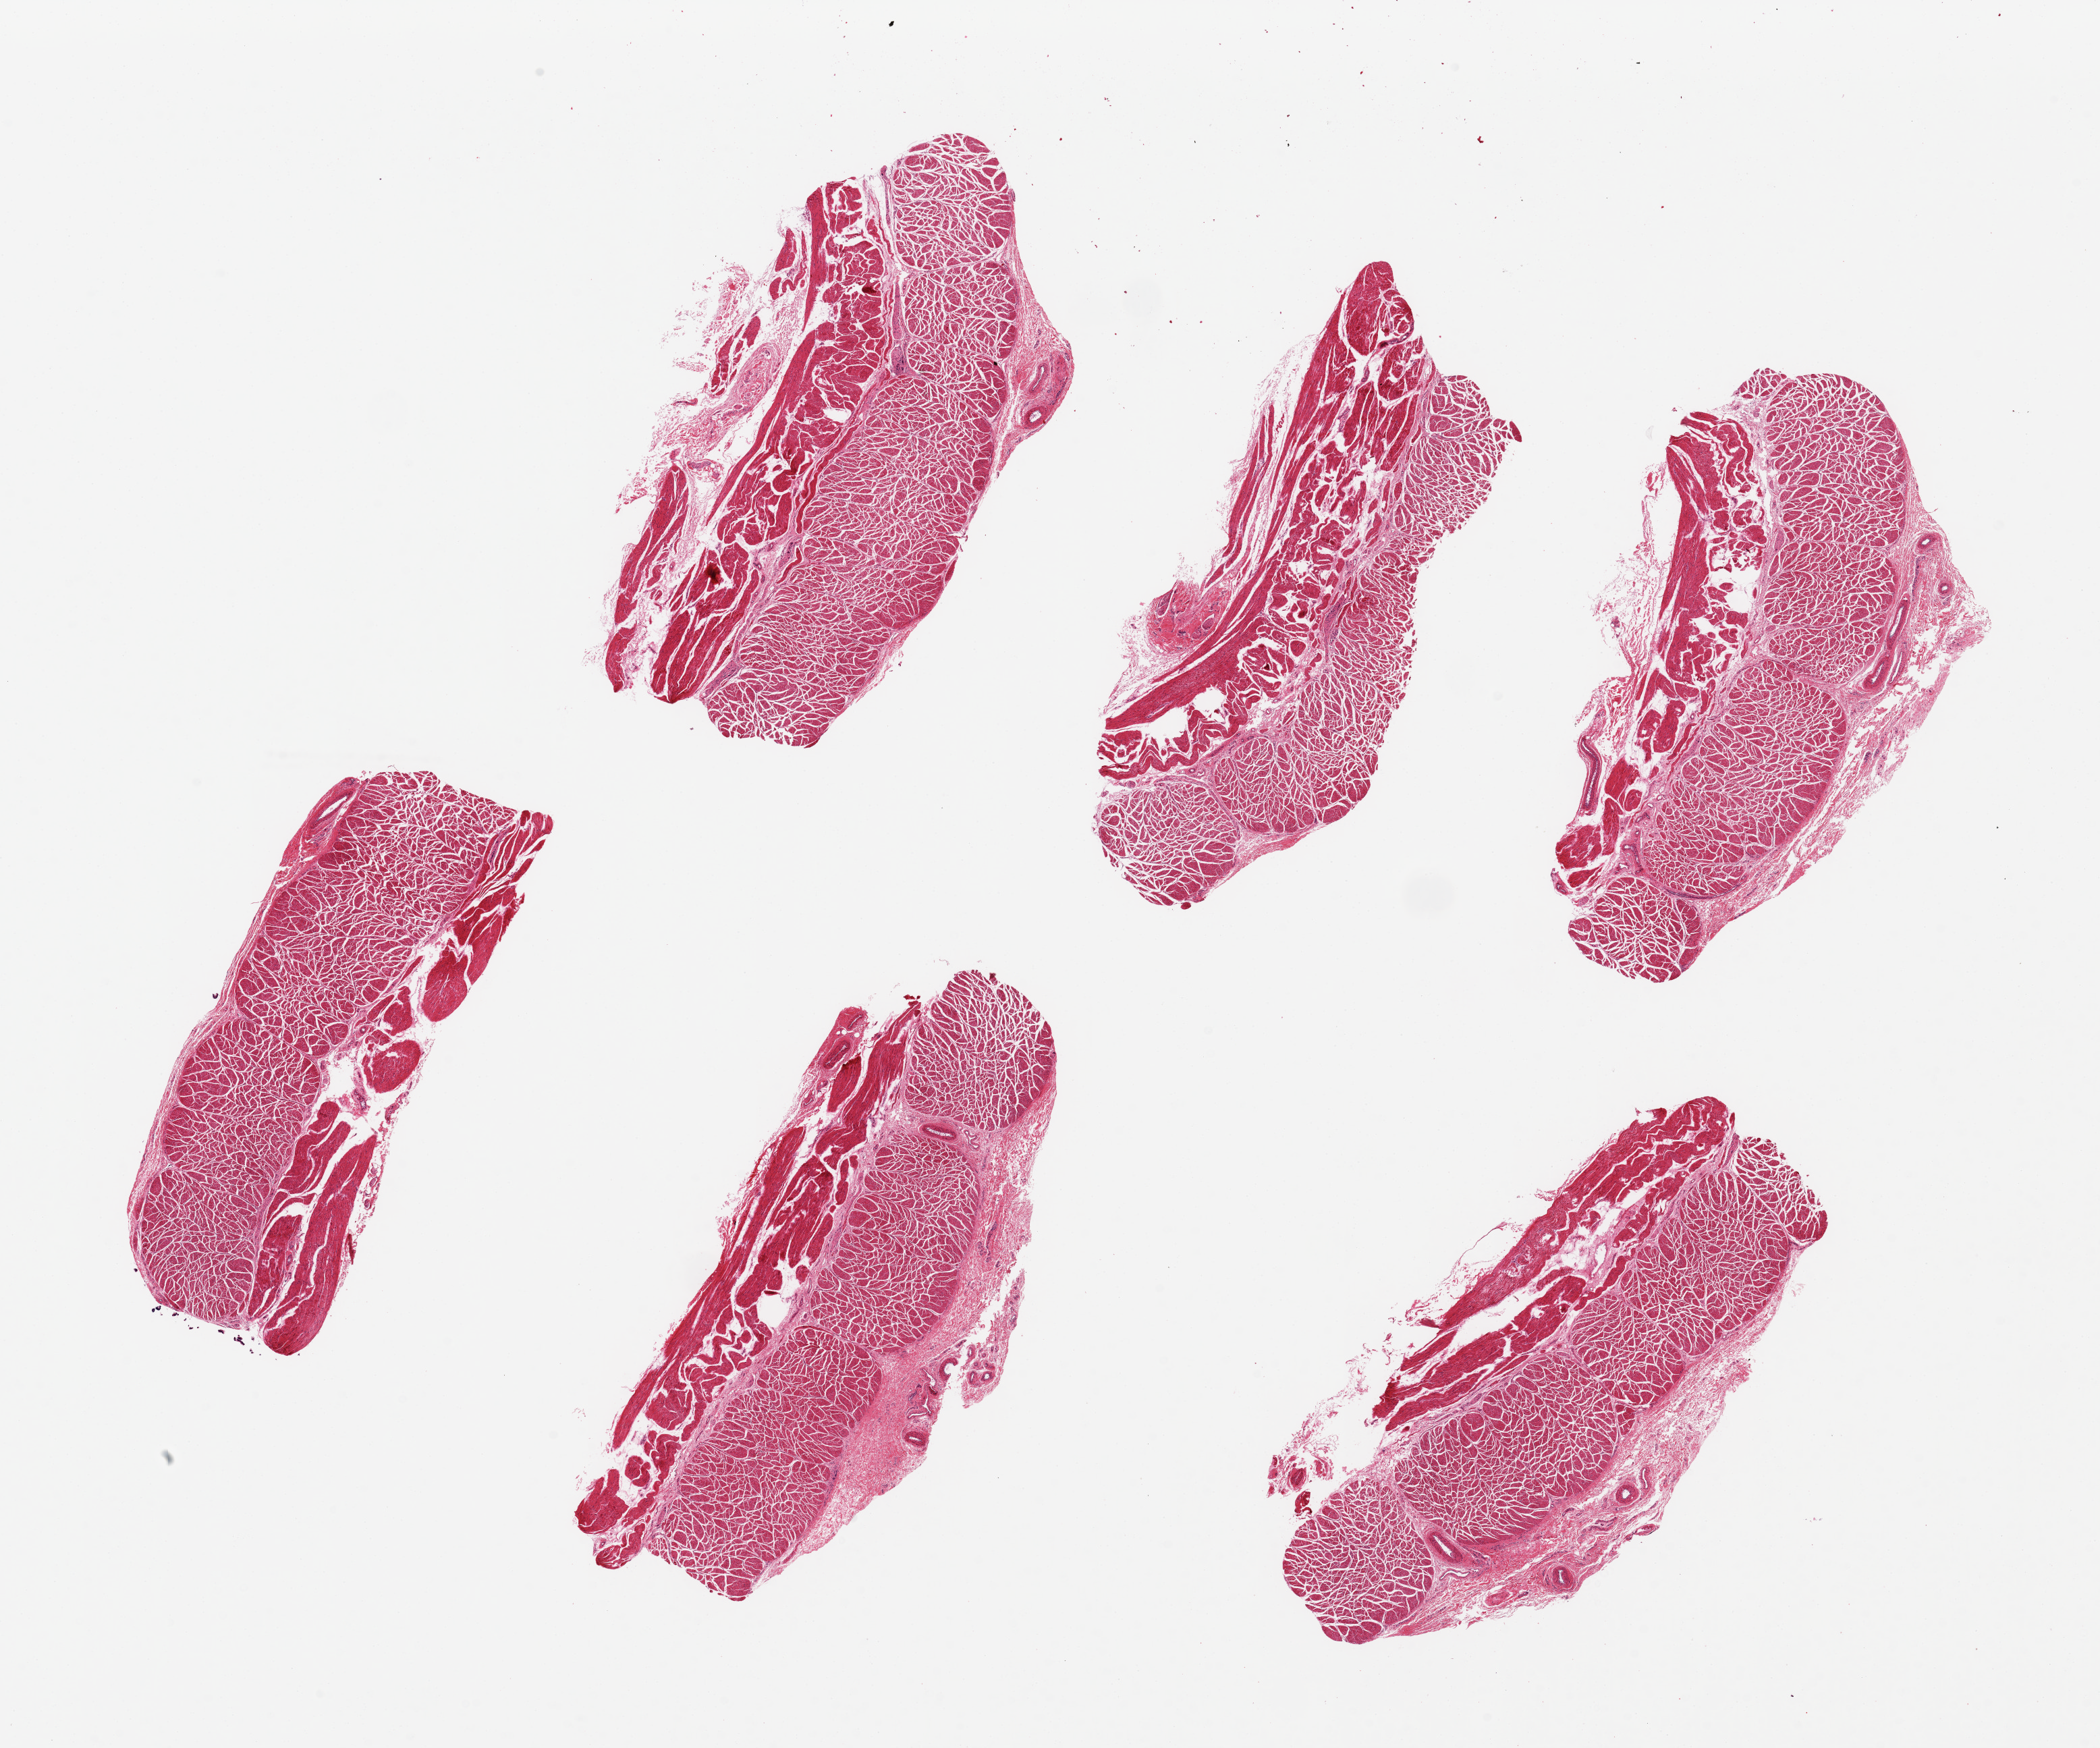
Hematoxylin and eosin (H&E) whole-slide image, shown as a low-resolution overview of the whole scanned area (about 24.6 x 20.5 mm, slide scanned at 20x), PAXgene-fixed paraffin-embedded (PFPE) section, section of esophageal muscle (target tissue), donor tissue sample. Donor: male.
Reviewer comment on this tissue sample: 6 pieces ~7x3.5mm.